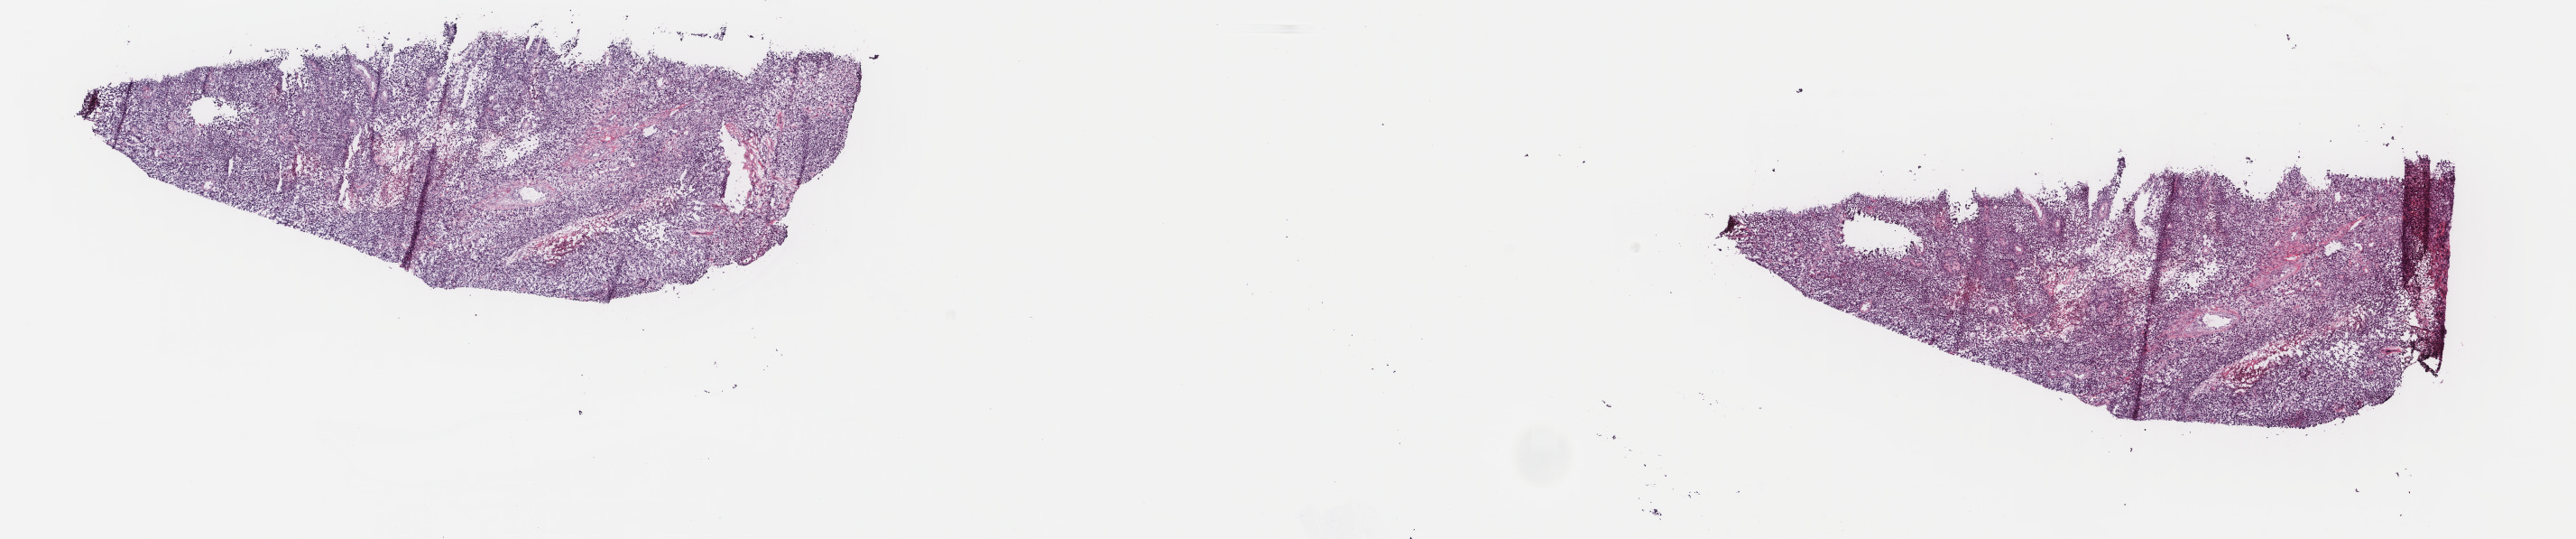
Whole-slide histology image, H&E-stained — shown as a low-resolution overview of the whole scanned area (about 22.7 x 4.7 mm). Frozen section from the top of the tissue portion. Metastatic tumour sample. Female, age 66 years at initial diagnosis. Composition of this section per pathologist review: tumour cells 75%, tumour nuclei 75%, normal cells 0%, stromal cells 16%, necrosis 9%. Inflammatory infiltration, as recorded: lymphocyte infiltration 7%, monocyte infiltration 1%, neutrophil infiltration 1%.
- this section: metastatic tumour tissue
- patient diagnosis: Amelanotic melanoma